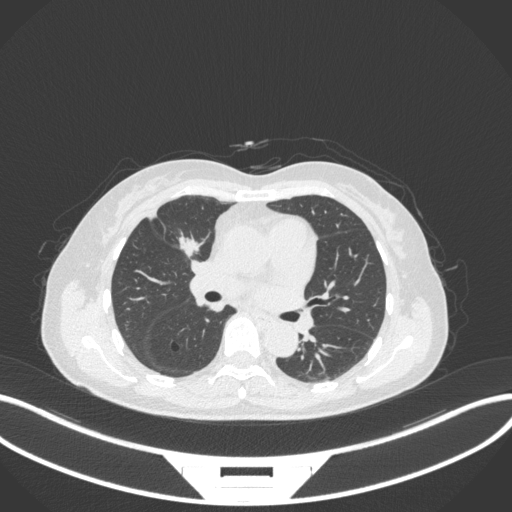
Chest CT, one axial slice; slice 165 of 282 in the series (ordered by position); 120 kVp; lung window (W 1500 / L -600 HU); 1 mm slice thickness; 512 × 512 image matrix, field of view 400 × 400 mm. Female patient, age 51 years. Case-level facts recorded for this patient, not image findings: clinical TNM (as recorded): T1c N0 M0.
Structures marked on this image (rectangle marked by the reading radiologist):
- lung tumour (recorded histology: adenocarcinoma): box from (x=172, y=230) to (x=209, y=262) px